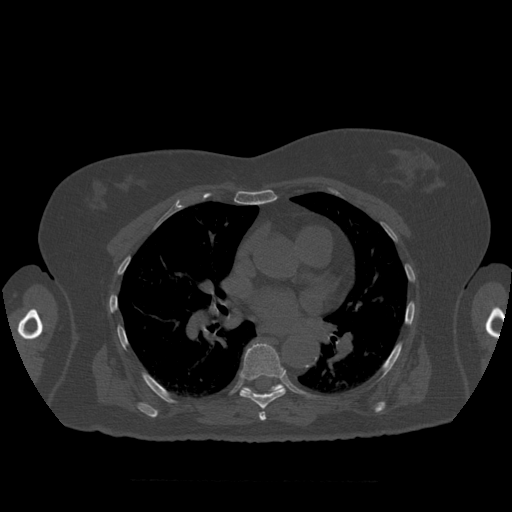
CT including the spine, one axial slice; slice 393 of 399 in the series (ordered by position); bone window (W 1800 / L 400 HU); 512 × 512 image matrix, field of view 404 × 404 mm. Patient age 81 years. From the clinical record (not read from this slice): primary cancer: renal; vertebrae with lytic lesions (as recorded): L1.
Structures marked on this image (semi-automatically segmented with operator editing):
- T7 vertebra: bounding box (x1, y1, x2, y2) in pixels: (240, 343, 286, 421)
- T8 vertebra: (242, 384, 285, 394)